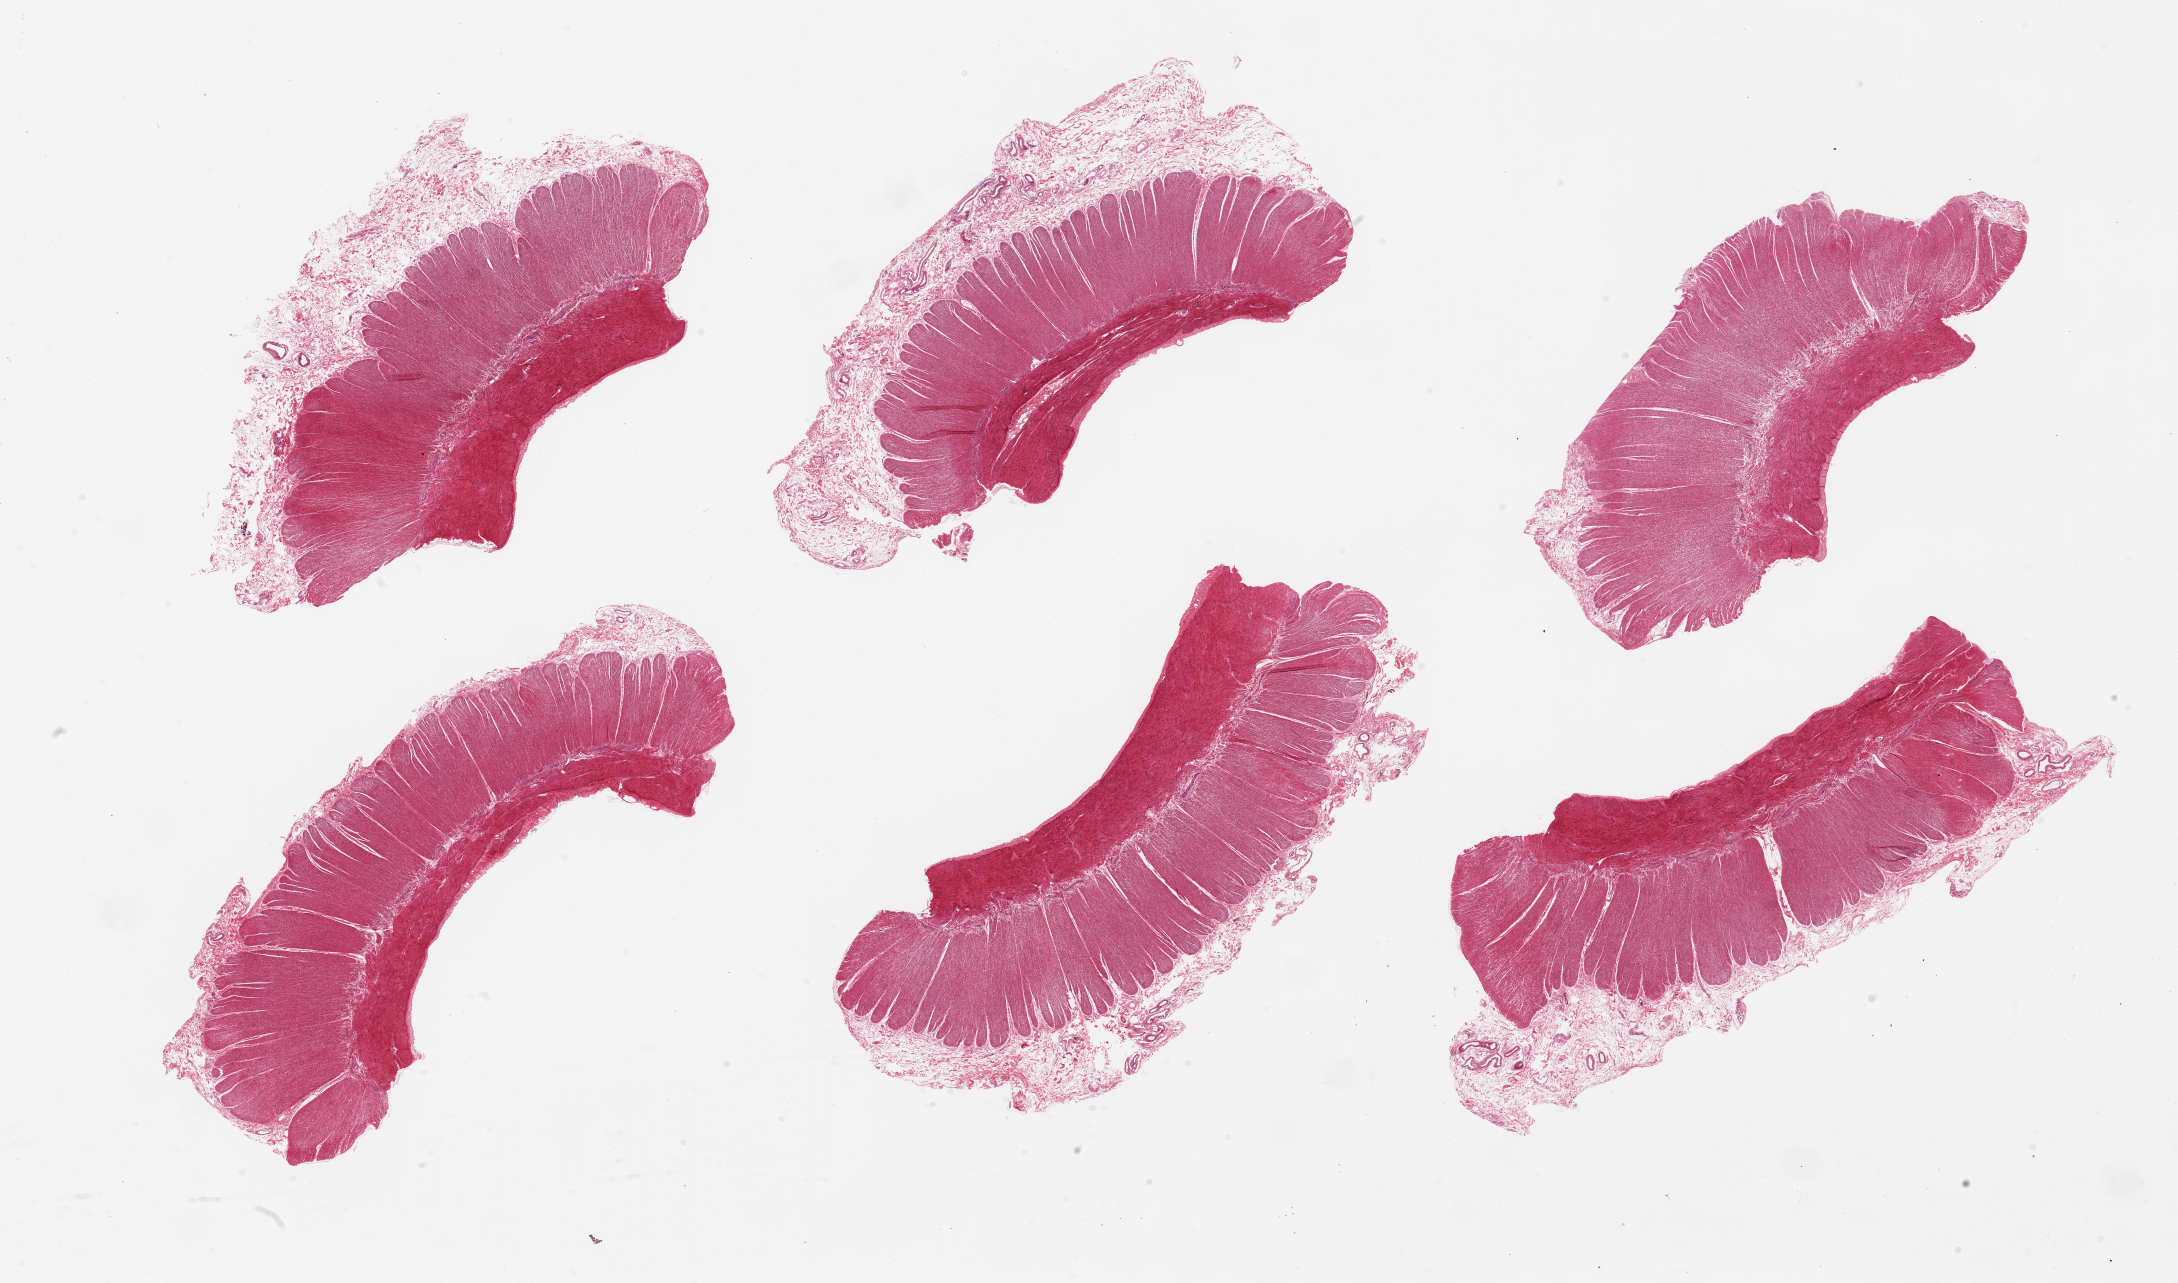
Whole-slide image, H&E stain, a low-resolution overview of the entire scanned area, about 34.5 x 20.3 mm (from a 20x scan). PAXgene-fixed paraffin-embedded (PFPE) section. Target tissue: sigmoid colon. Tissue donor sample.
Reviewer comment on this tissue sample: 6 pieces; muscularis and residual submucosa.